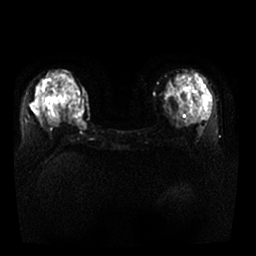
Breast MRI, one axial slice; position 15 of 29 along the scan axis; diffusion-weighted series; image 2 of 4 stored at this slice position (different b-values; order by instance number); 1.5 T; 4 mm slice thickness; 256 × 256 image matrix. Female patient.
Annotated regions visible in this slice (outlined manually by an expert reader):
- tumour on diffusion-weighted imaging: box from (x=74, y=106) to (x=87, y=131) px